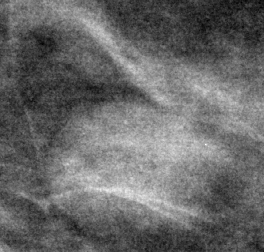
Crop from a digitized film mammogram around one marked abnormality; right breast; CC view; BI-RADS breast density category 2 (scale 1–4).
Mass, shape oval, margins circumscribed; BI-RADS assessment category 3; pathology result (as recorded, not read from the image): benign.